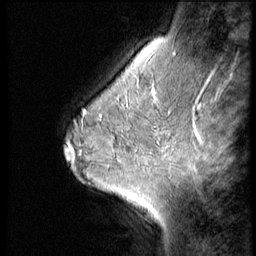
Breast MRI (dynamic contrast-enhanced), one sagittal slice; slice 42 of 56 in the series (ordered by position); 3 images stored at this slice position (order not interpretable as contrast timing); 1.5 T; TE 4.2 ms, TR 9 ms; 256 × 256 image matrix, field of view 180 × 180 mm. Patient: female, 45 years. Case-level facts recorded for this patient, not image findings: setting: breast cancer imaged before/during neoadjuvant chemotherapy; receptor status: HR-positive, HER2-negative.
Annotated regions visible in this slice (semi-automatic segmentation, software-assisted and operator-edited):
- analysis volume of interest (the breast-tissue region the enhancement analysis was run in; not a lesion): bounding box (x1, y1, x2, y2) in pixels: (102, 77, 166, 129)
- tumour enhancement mask (voxels above the 140 % enhancement threshold inside the analysis volume of interest): (150, 88, 158, 102)